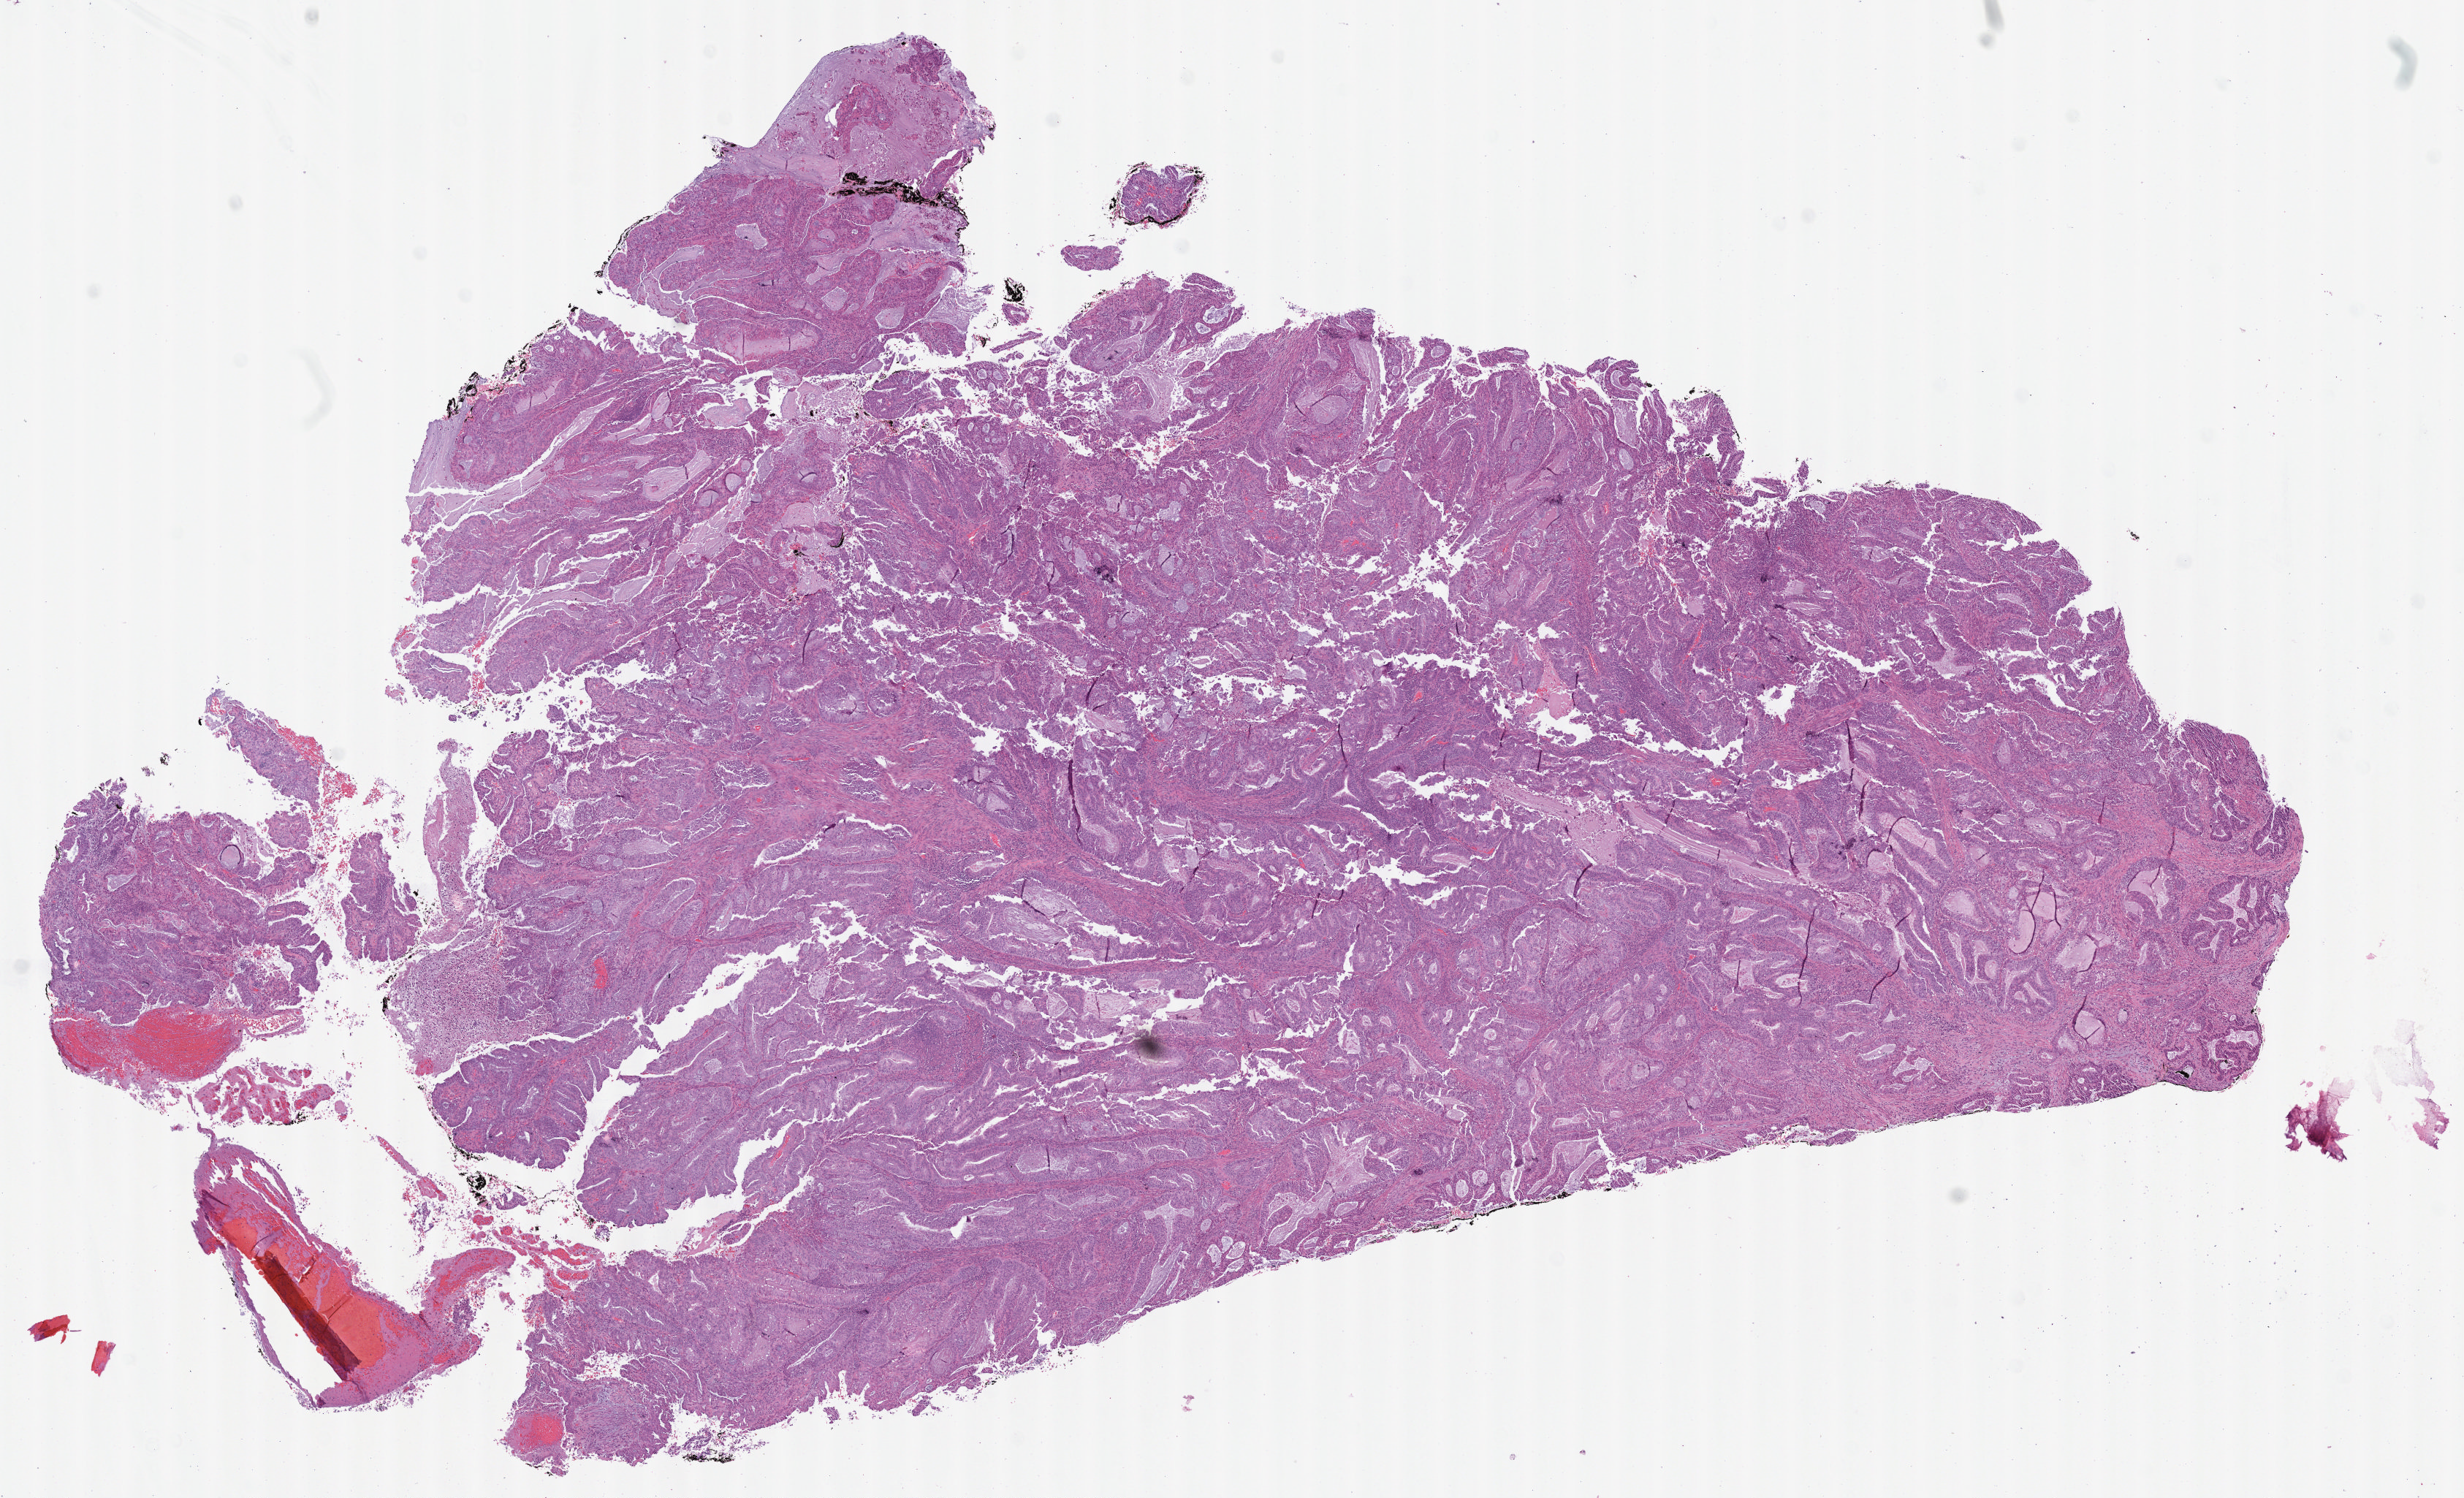
Whole-slide histology image, H&E — whole scanned area (about 13.6 x 8.3 mm, from a 40x scan) shown as a low-resolution overview, formalin-fixed paraffin-embedded (FFPE) diagnostic section, primary tumour sample from the uterus. Female patient; age at initial diagnosis 54 years. Histologic grade: G3 (poorly differentiated).
Histologic diagnosis: Endometrioid adenocarcinoma, NOS (endometrium). FIGO stage: II.